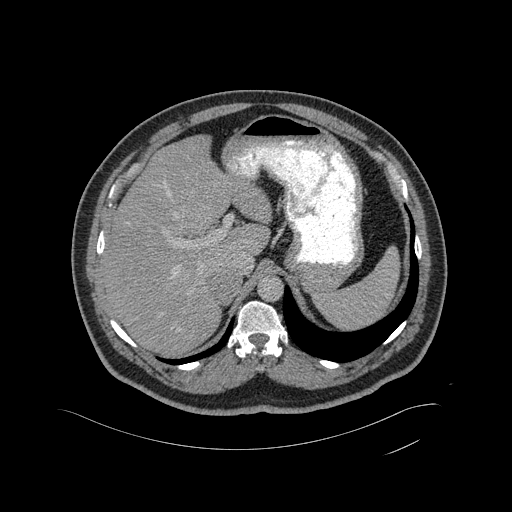
Contrast-enhanced abdominal CT, one axial slice. Slice 342 of 433 in the series (ordered by position). 120 kVp. Intravenous contrast given. Soft-tissue window (W 400 / L 40 HU). 512 × 512 image matrix, field of view 500 × 500 mm. Male patient, age 56 years. Case-level facts recorded for this patient, not image findings: diagnosis: adrenocortical carcinoma; tumour side: right adrenal; tumour size at pathology: 11.6 cm; Ki-67 index: 50 %; stage (as recorded): 3.
Outlined on this slice (semi-automatic segmentation, software-assisted and operator-edited):
- mass: box from (x=212, y=271) to (x=239, y=302) px